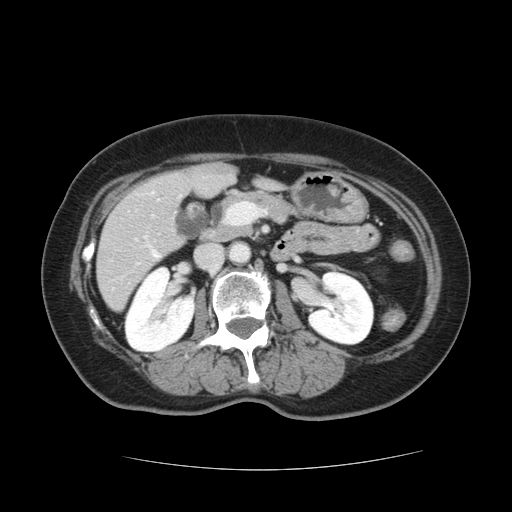
Contrast-enhanced abdominal CT, one axial slice. Position 48 of 128 along the scan axis. 120 kVp. Intravenous contrast given. Soft-tissue window (W 400 / L 40 HU). 2.5 mm slice thickness. 512 × 512 image matrix. Female patient, age 67 years. From the clinical record (not read from this slice): diagnosis: colorectal cancer liver metastases, imaged before liver resection; multiple liver metastases: yes; largest metastasis: 3 cm; disease in both lobes: yes.
Outlined on this slice (manually delineated by an expert):
- hepatic veins: bounding box [x1, y1, x2, y2] px = [152, 251, 159, 257]
- liver: [98, 164, 236, 310]
- planned liver remnant (the part of the liver to remain after resection): [98, 221, 180, 310]